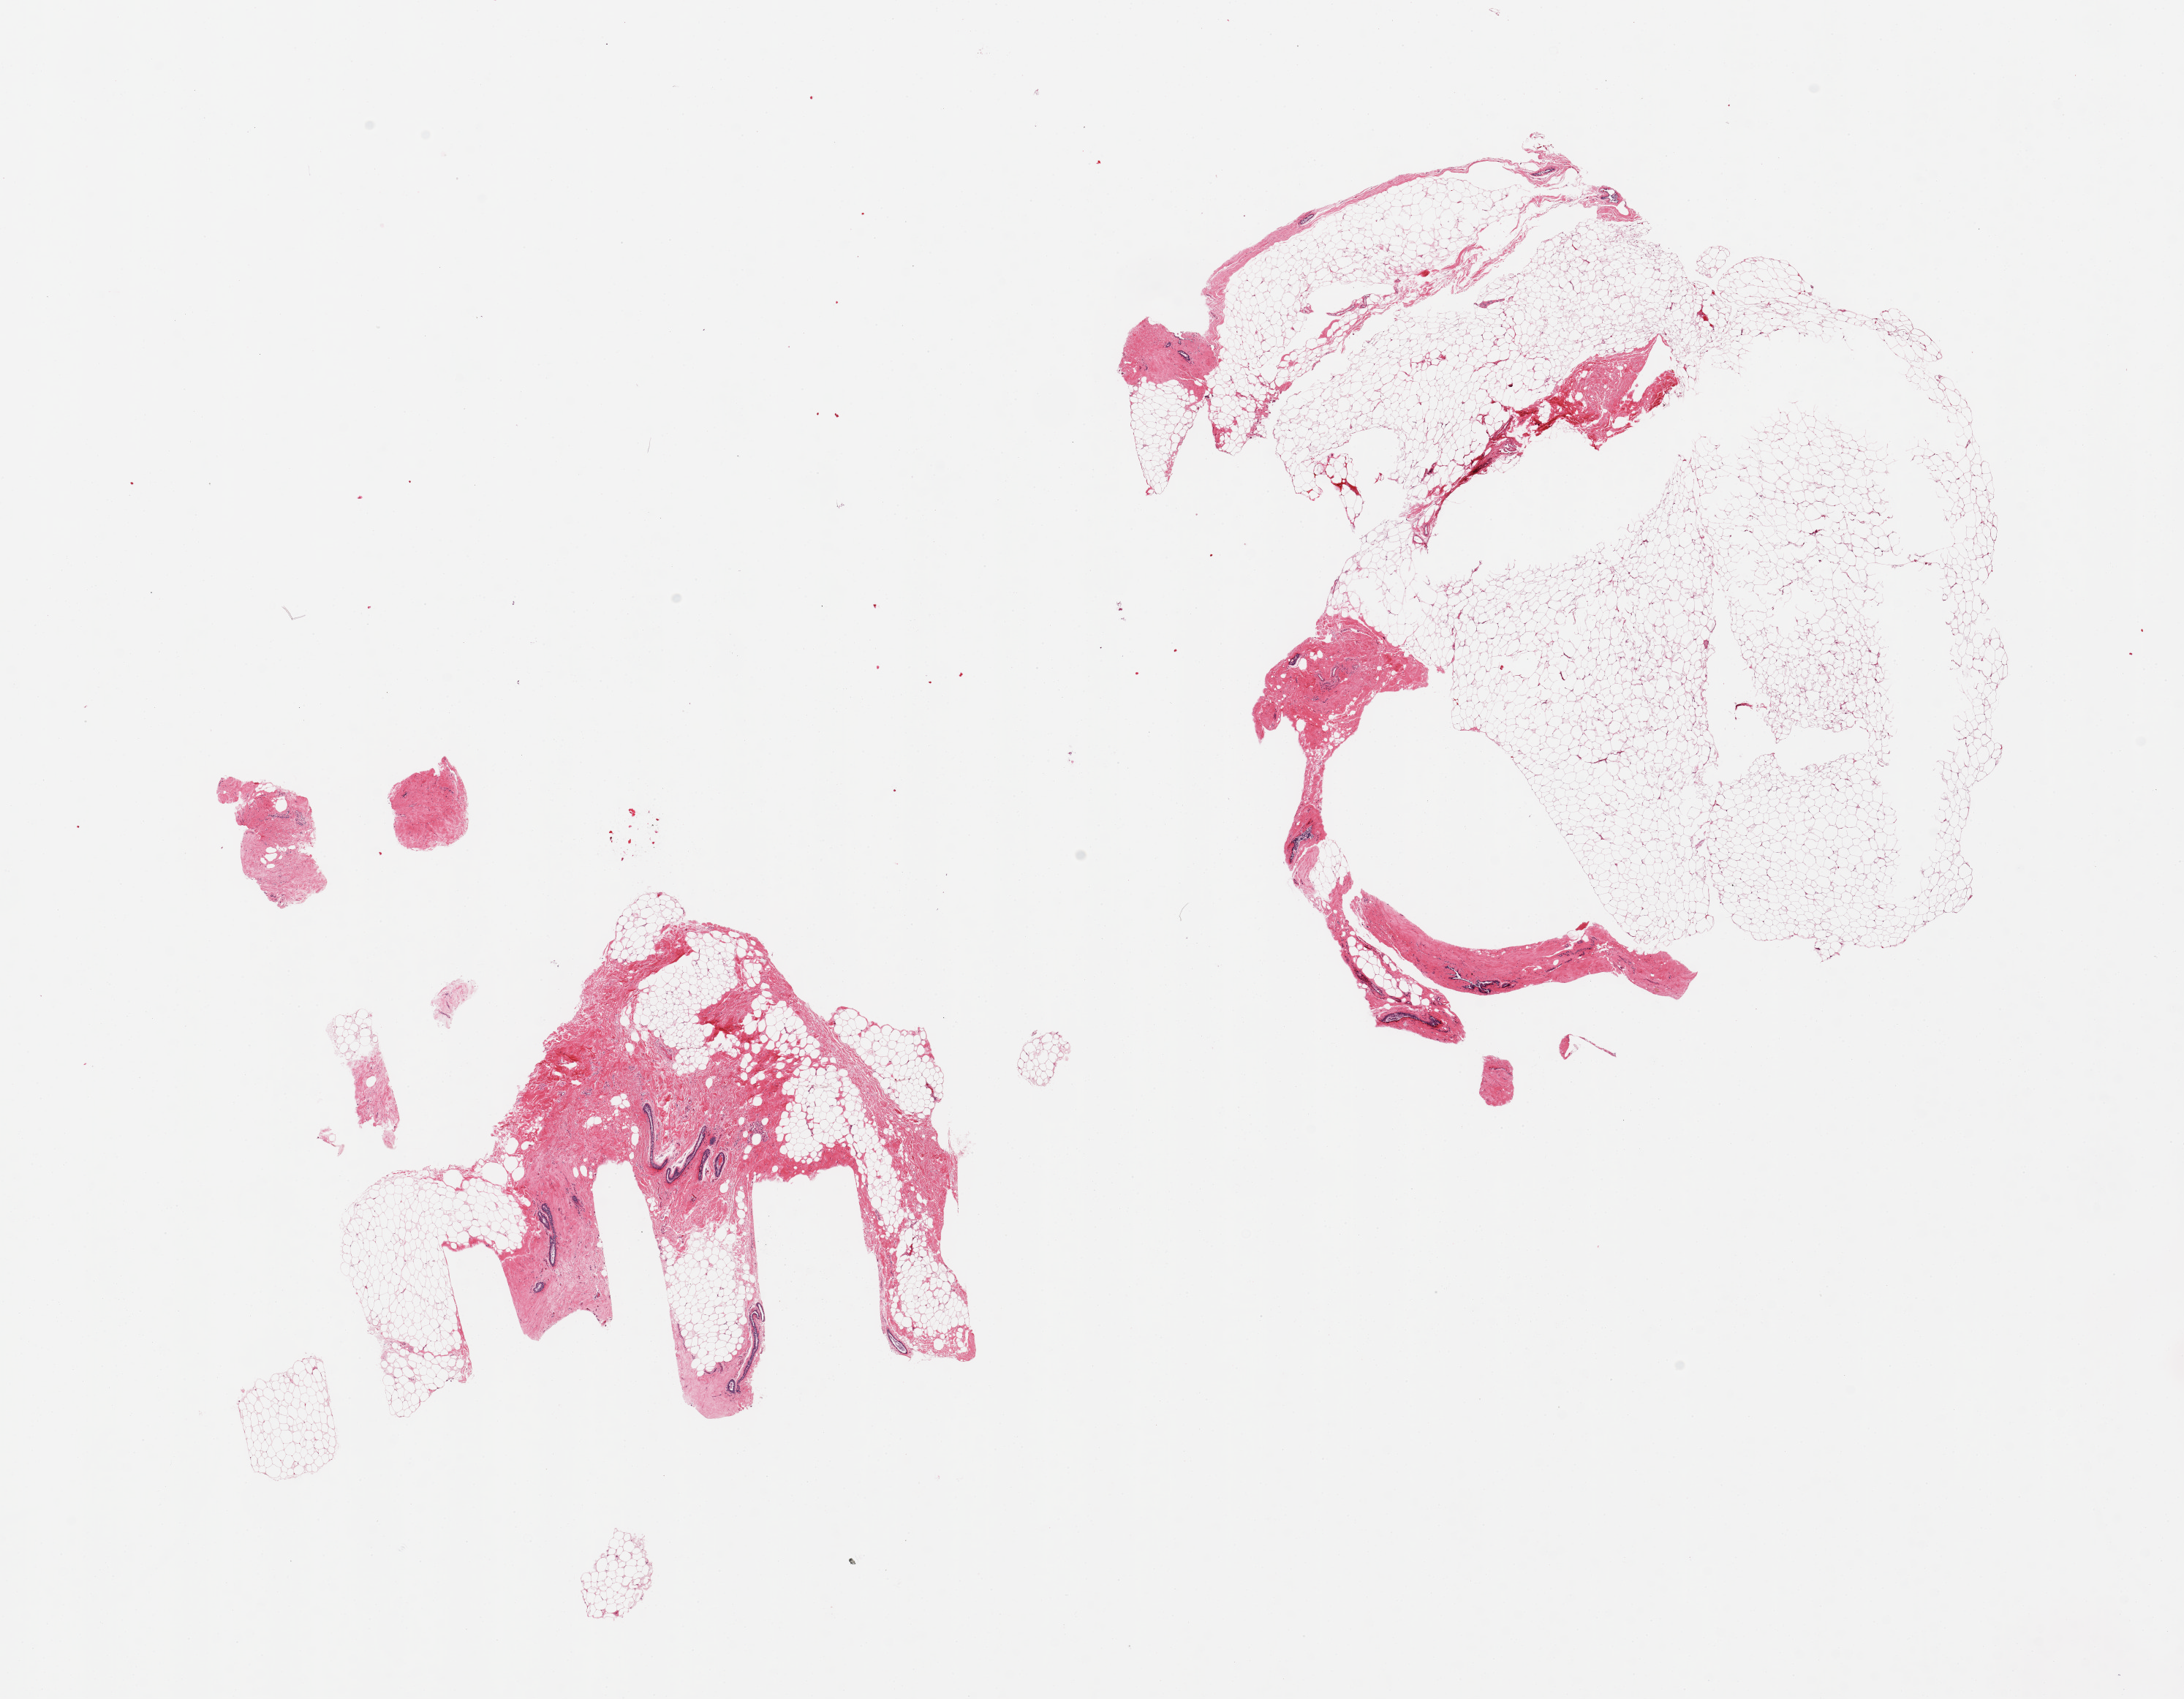
Haematoxylin and eosin whole-slide image — a low-resolution overview of the entire scanned area, about 23.6 x 18.4 mm (slide scanned at 20x); PAXgene-fixed, paraffin-embedded tissue; sampled site (target tissue): breast; tissue donor sample. Donor sex: male.
• pathologist's review note for this sample: 2 pieces; ducts in fibroadipose tissue